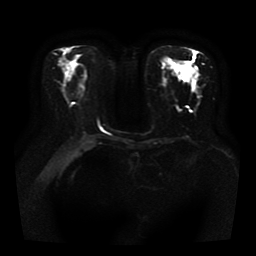
Breast MRI, one axial slice. Position 18 of 41 along the scan axis. Diffusion-weighted series; image 2 of 4 stored at this slice position (different b-values; order by instance number). 1.5 T. 5 mm slice thickness. 256 × 256 image matrix, field of view 330 × 330 mm. Female patient.
Structures marked on this image (expert manual segmentation):
- tumour on diffusion-weighted imaging: bounding box [x1, y1, x2, y2] px = [185, 69, 195, 77]